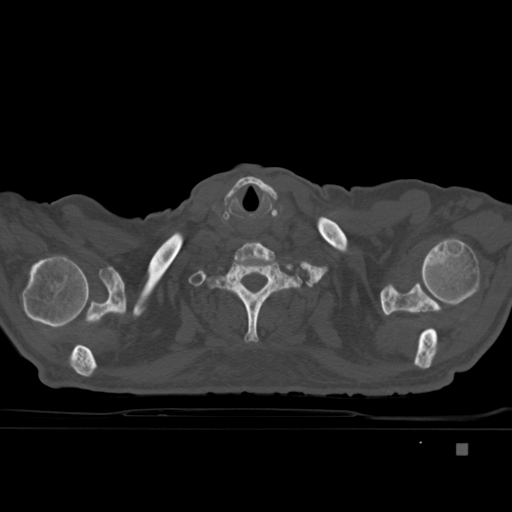
CT including the spine, one axial slice; position 360 of 451 along the scan axis; bone window (W 1800 / L 400 HU); 512 × 512 image matrix. Patient: male, 75 years. From the clinical record (not read from this slice): primary cancer: prostate.
Structures marked on this image (semi-automatically segmented with operator editing):
- T1 vertebra: bounding box <200,256,302,343> (left, top, right, bottom; pixels)